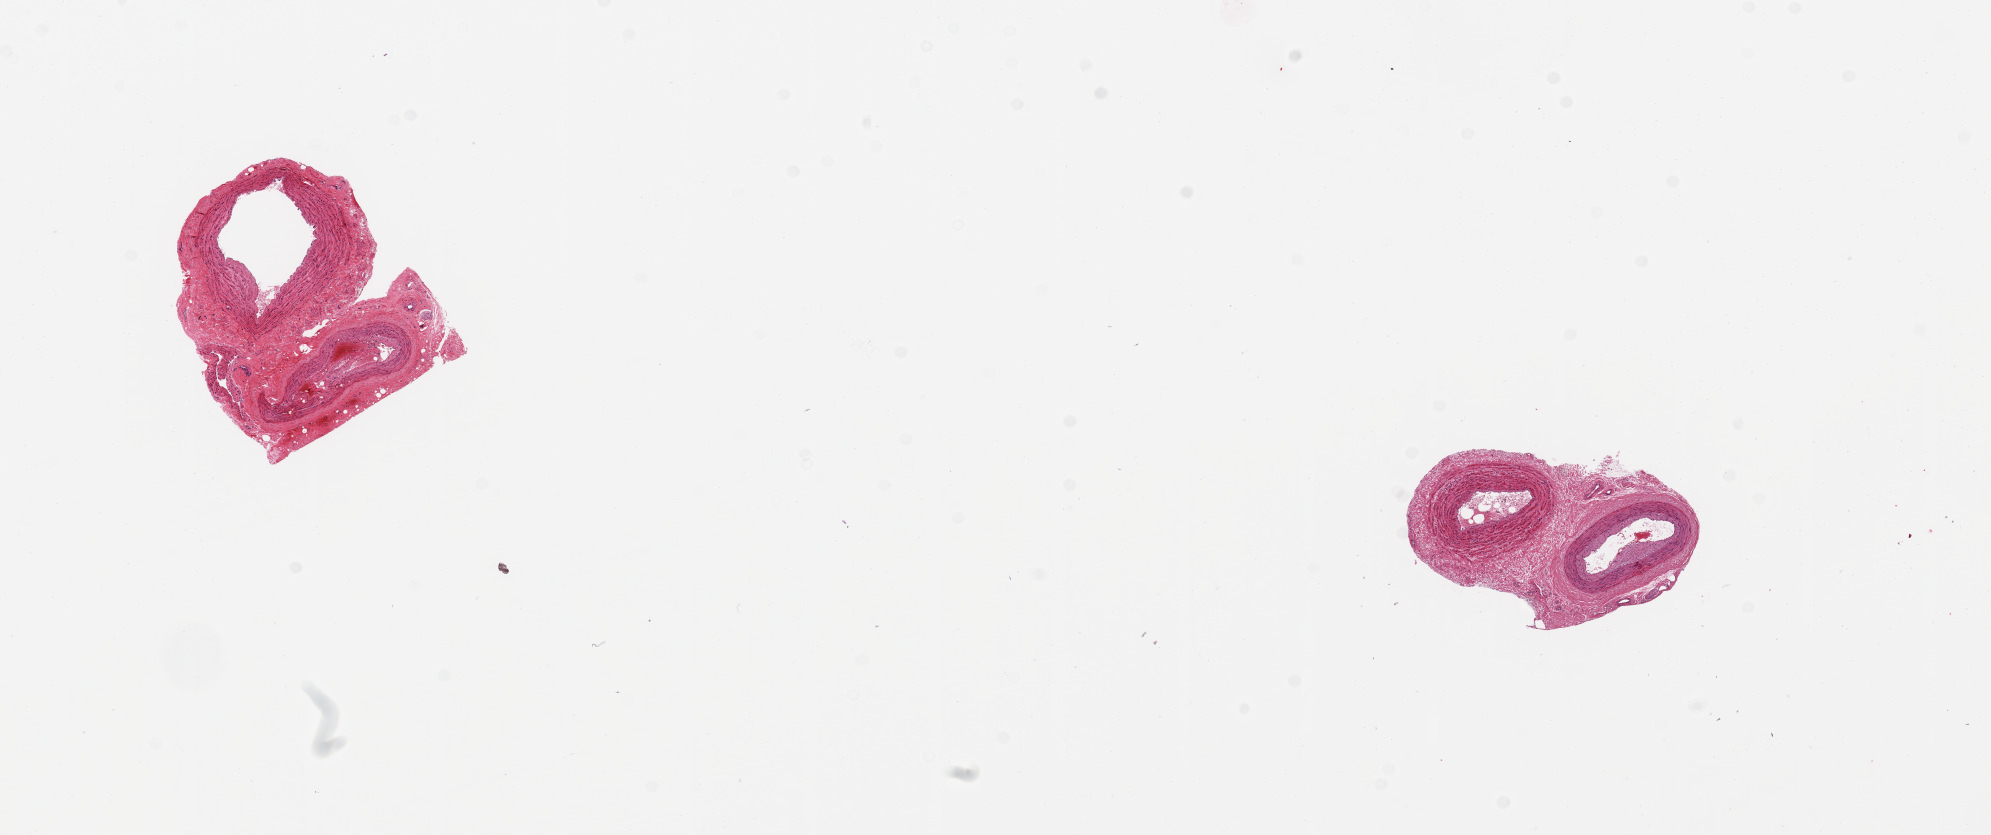
Hematoxylin and eosin (H&E) whole-slide image — low-resolution overview of the scanned area, about 15.8 x 6.6 mm (acquisition: 20x scan); PAXgene-fixed, paraffin-embedded tissue; section of tibial artery (target tissue); donor tissue sample. Donor sex: female.
Review note (as recorded): 2 pieces of 2 small arteries joined by connective tissue, each ~1mm in diameter. Focal atherosis.